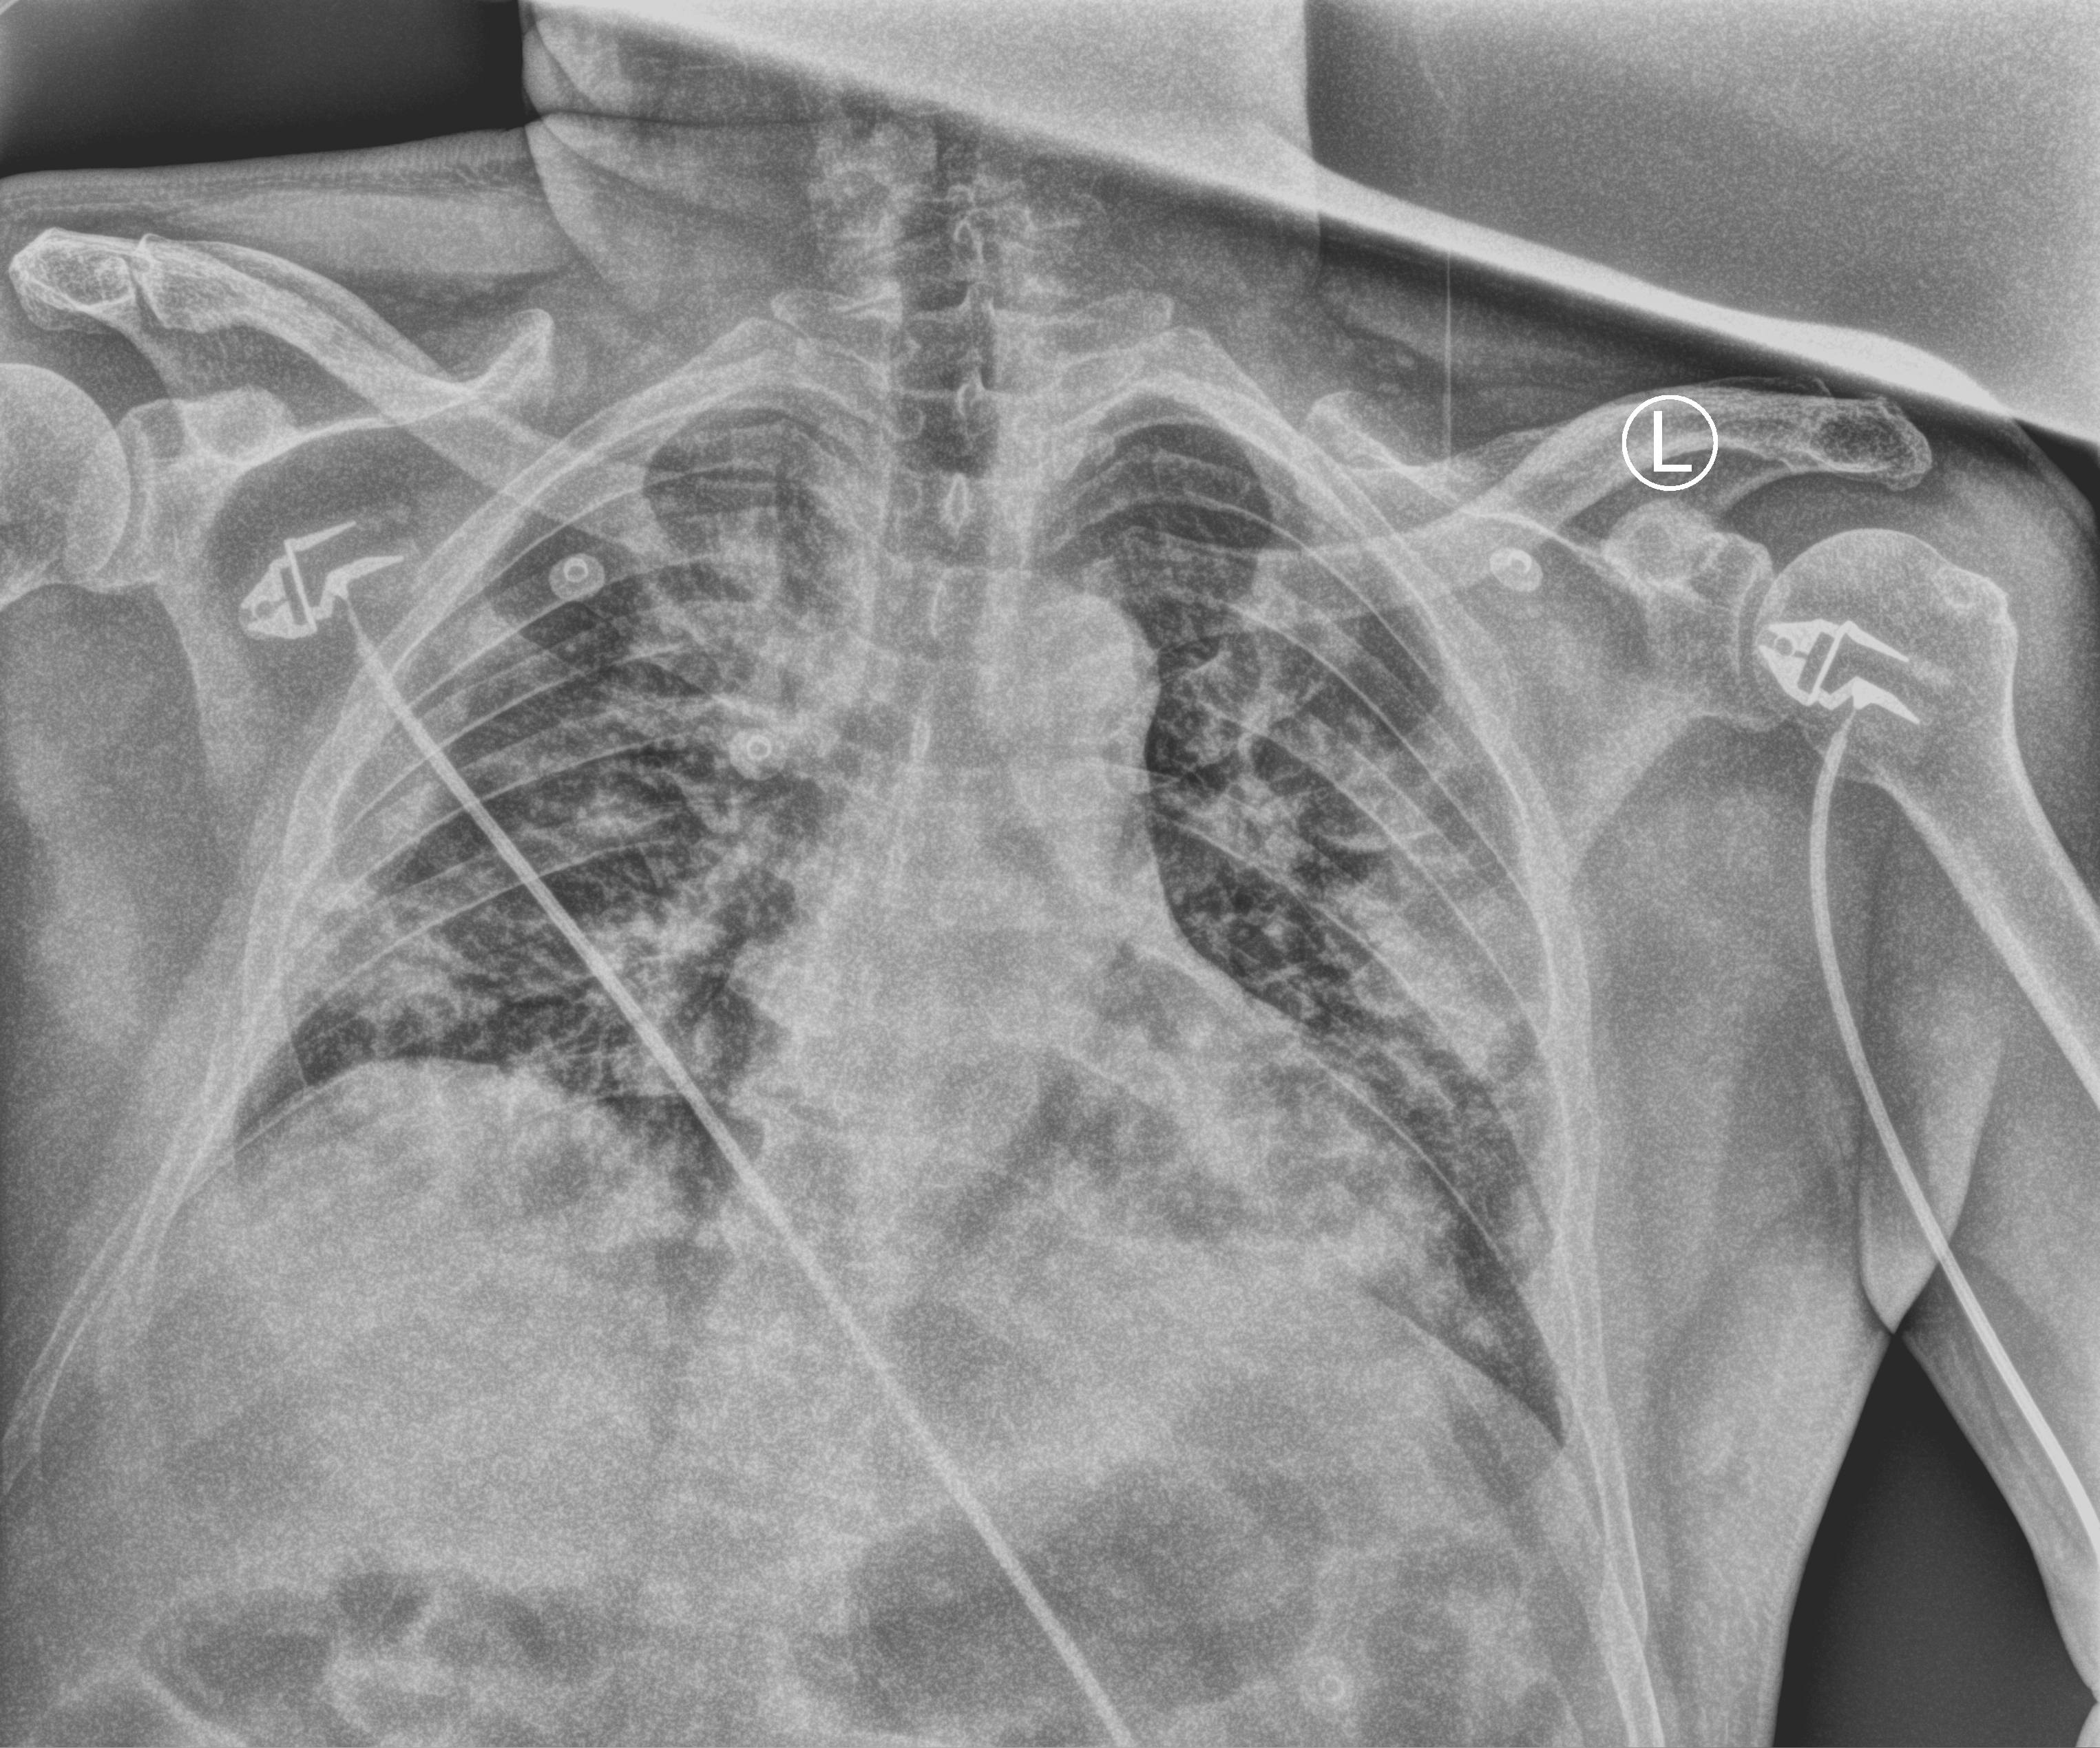
Portable chest radiograph; anteroposterior (AP) projection. Male patient hospitalised with COVID-19, age 60–74 years.
From the hospital-stay record, not from the radiograph (when in the stay this image was taken is not recorded): mechanically ventilated during this hospital stay: no; admitted to intensive care during this hospital stay: no.